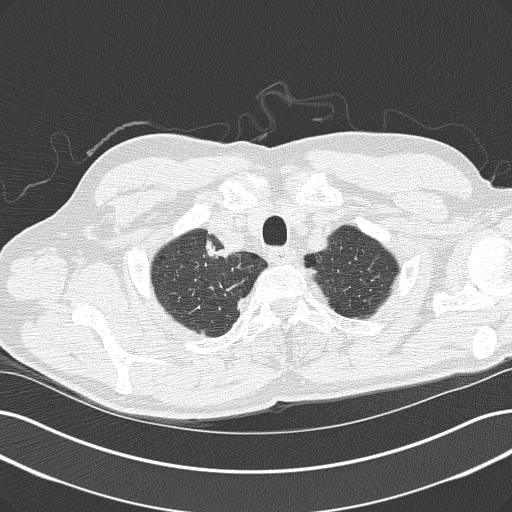
Axial slice from a low-dose chest CT screening exam; baseline annual screen; lung window (W 1500 / L -600 HU); lung (sharp) reconstruction kernel (B50f); slice 21 of 152 in the series; 512 × 512 image matrix. Male, age 61 years at enrolment.
- Expert-annotated lung lesion, box from (x=194, y=229) to (x=246, y=273) px.
- The screening reader recorded 2 non-calcified nodules or masses ≥4 mm on this exam (right upper lobe, right upper lobe); which of them this box marks is not recorded.
- Official screen result: positive, change unspecified: nodule(s) >= 4 mm or enlarging nodule(s), mass(es), or other non-specific abnormalities suspicious for lung cancer.
- Participant outcome: lung cancer diagnosed 54 days after this screen — adenocarcinoma, NOS, right upper lobe, poorly differentiated (G3), stage IIIB (AJCC 6th edition).